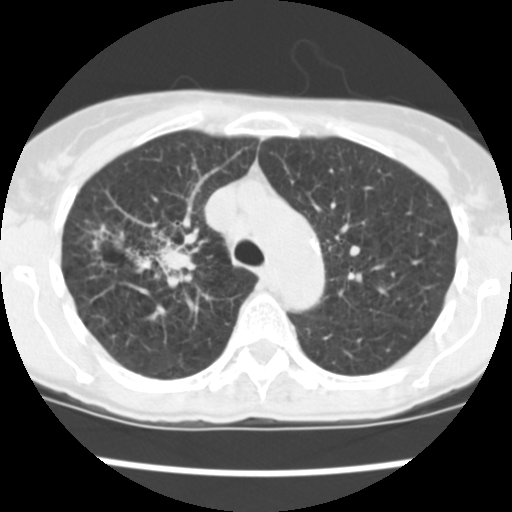
Low-dose screening chest CT, one axial slice. Slice 178 of 252 in the series (ordered by position). Reconstruction kernel STANDARD. 120 kVp. Lung window (W 1500 / L -600 HU). 512 × 512 image matrix, field of view 276 × 276 mm.
Annotated regions visible in this slice (manually delineated by an expert):
- lesion 2 (tumor, lower lobe of right lung): box from (x=135, y=242) to (x=196, y=280) px